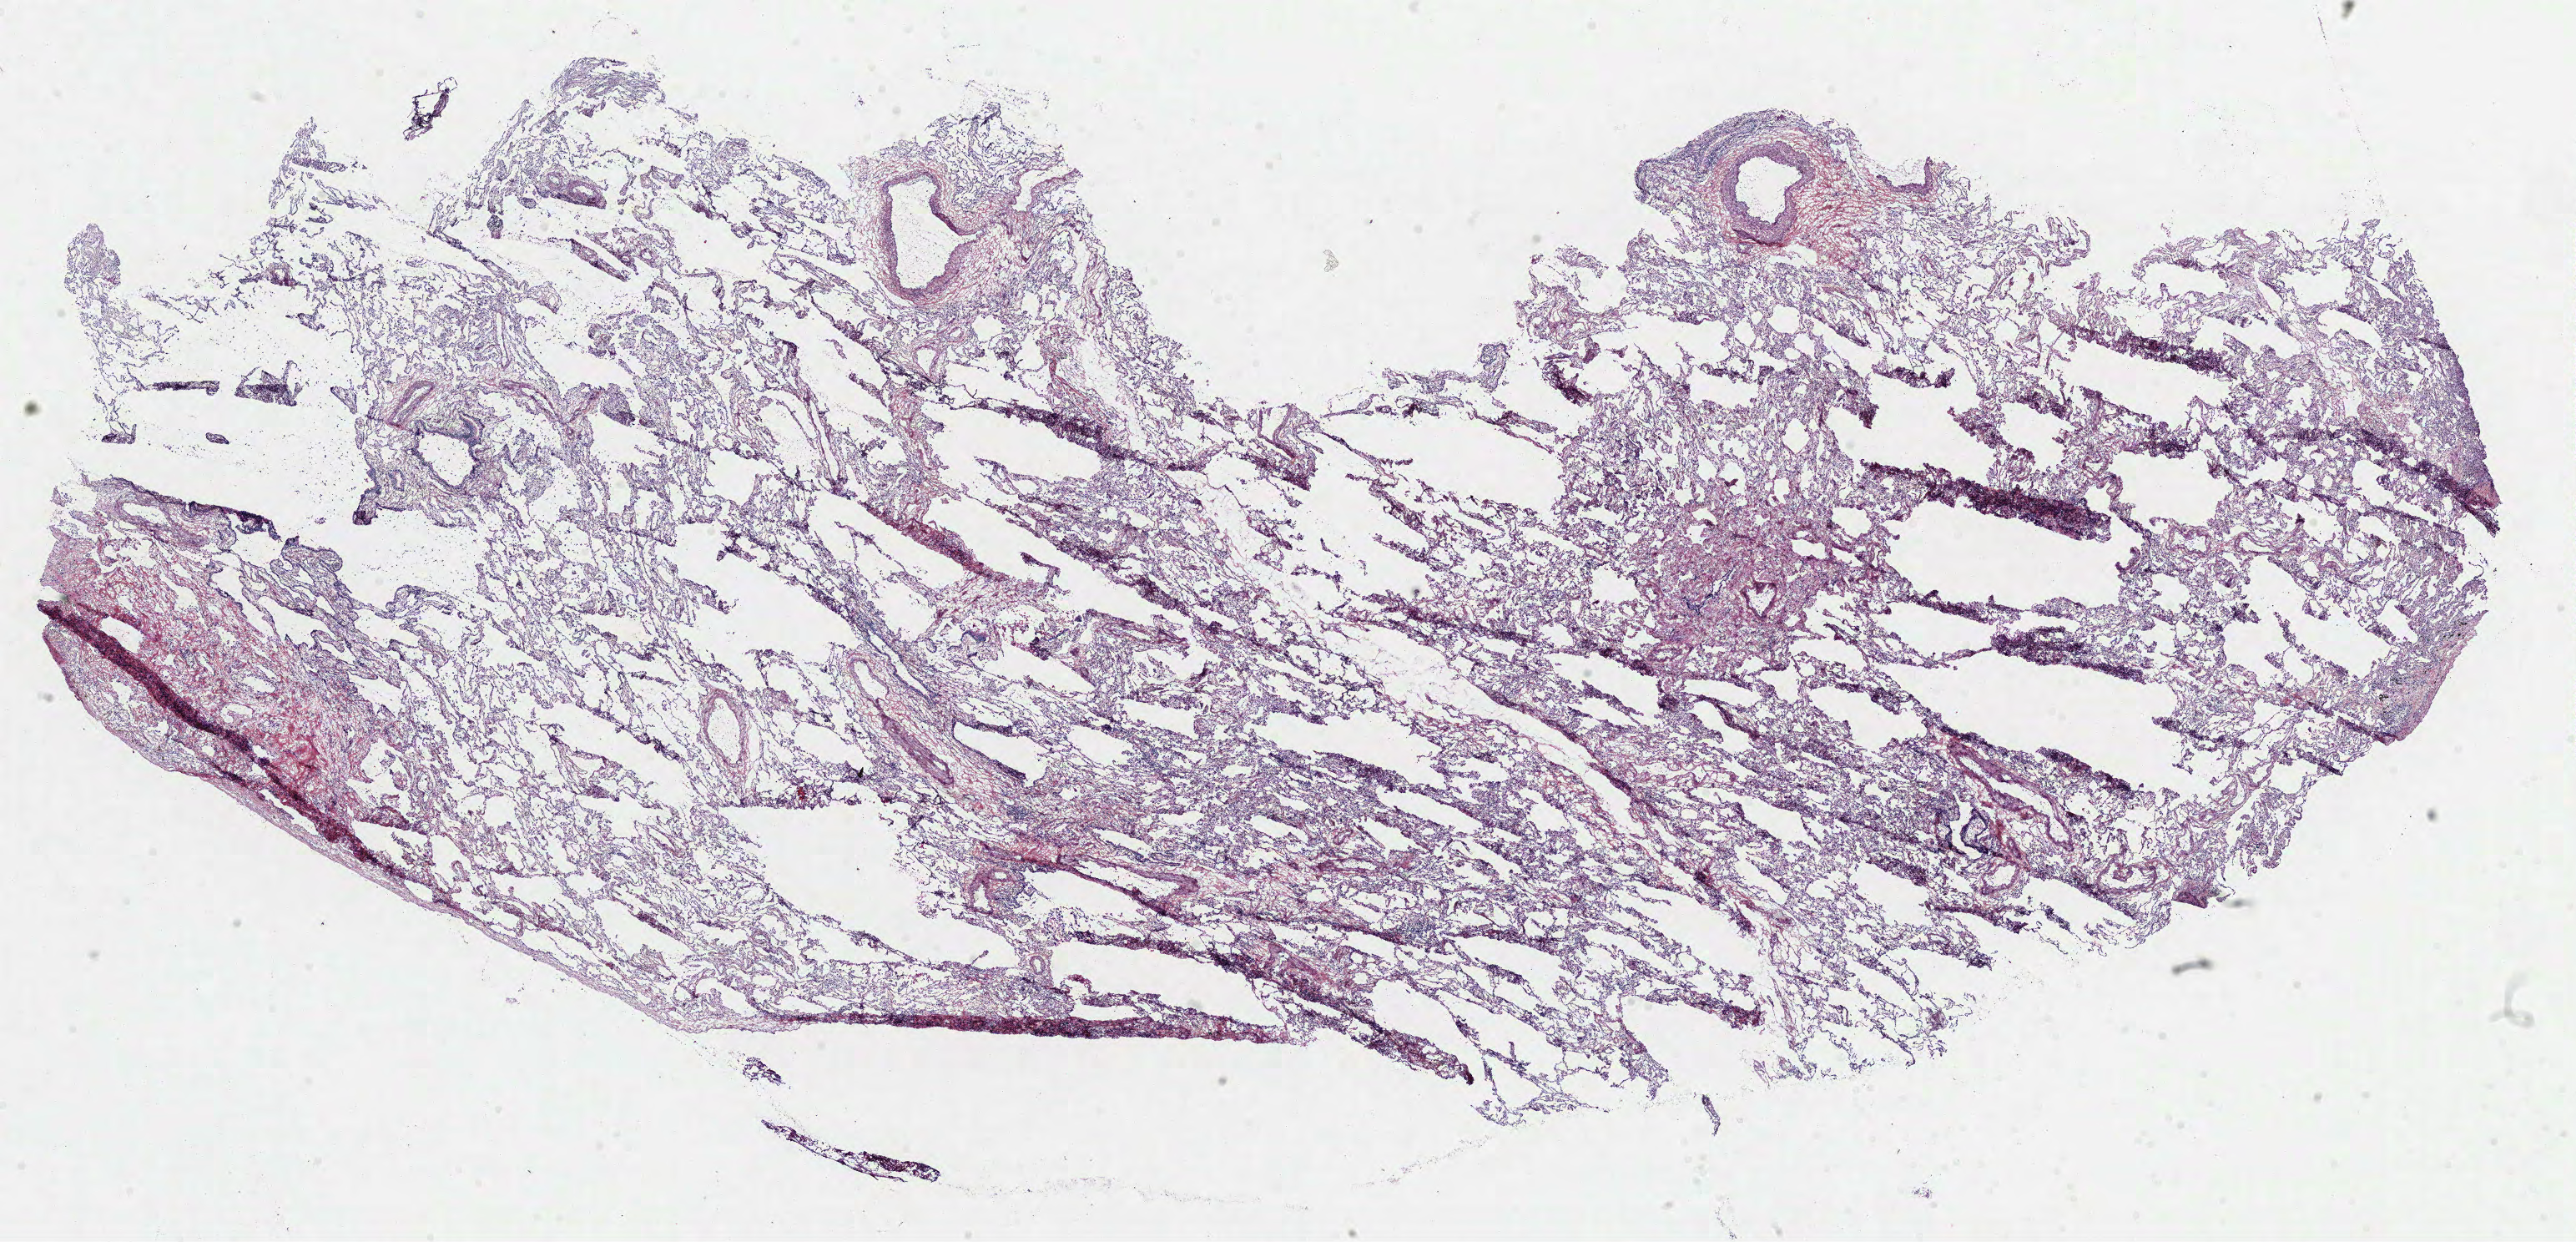
Digitized H&E tissue section (whole slide), whole scanned area (about 24.9 x 12.0 mm, slide scanned at 40x) shown as a low-resolution overview; frozen section from the top of the tissue portion; lung, solid tissue normal (non-tumour tissue) sample. Male, age 71 years at initial diagnosis.
- this section: solid tissue normal (non-tumour) sample from the same patient
- patient diagnosis: Squamous cell carcinoma, NOS (upper lobe, lung)